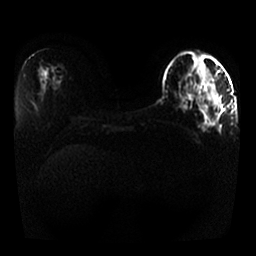
Breast MRI, one axial slice; position 12 of 25 along the scan axis; diffusion-weighted series; image 2 of 4 stored at this slice position (different b-values; order by instance number); 1.5 T; 4 mm slice thickness; 256 × 256 image matrix. Female patient.
Annotated regions visible in this slice (outlined manually by an expert reader):
- tumour on diffusion-weighted imaging: bounding box <210,94,219,104> (left, top, right, bottom; pixels)